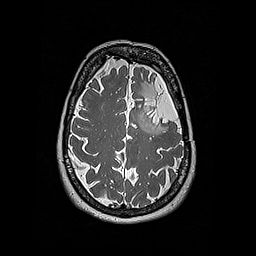
Brain MRI from a brain-tumour surgery series, one axial slice. Slice 135 of 192 in the series (ordered by position). 1 mm slice thickness. 256 × 256 image matrix, field of view 250 × 250 mm. Case-level facts recorded for this patient, not image findings: histopathology: Oligodendroglioma; WHO grade: 2; IDH mutation: yes; tumour location: Left Frontal.
Structures marked on this image (expert manual segmentation):
- tumour: bounding box (x1, y1, x2, y2) in pixels: (137, 85, 158, 133)